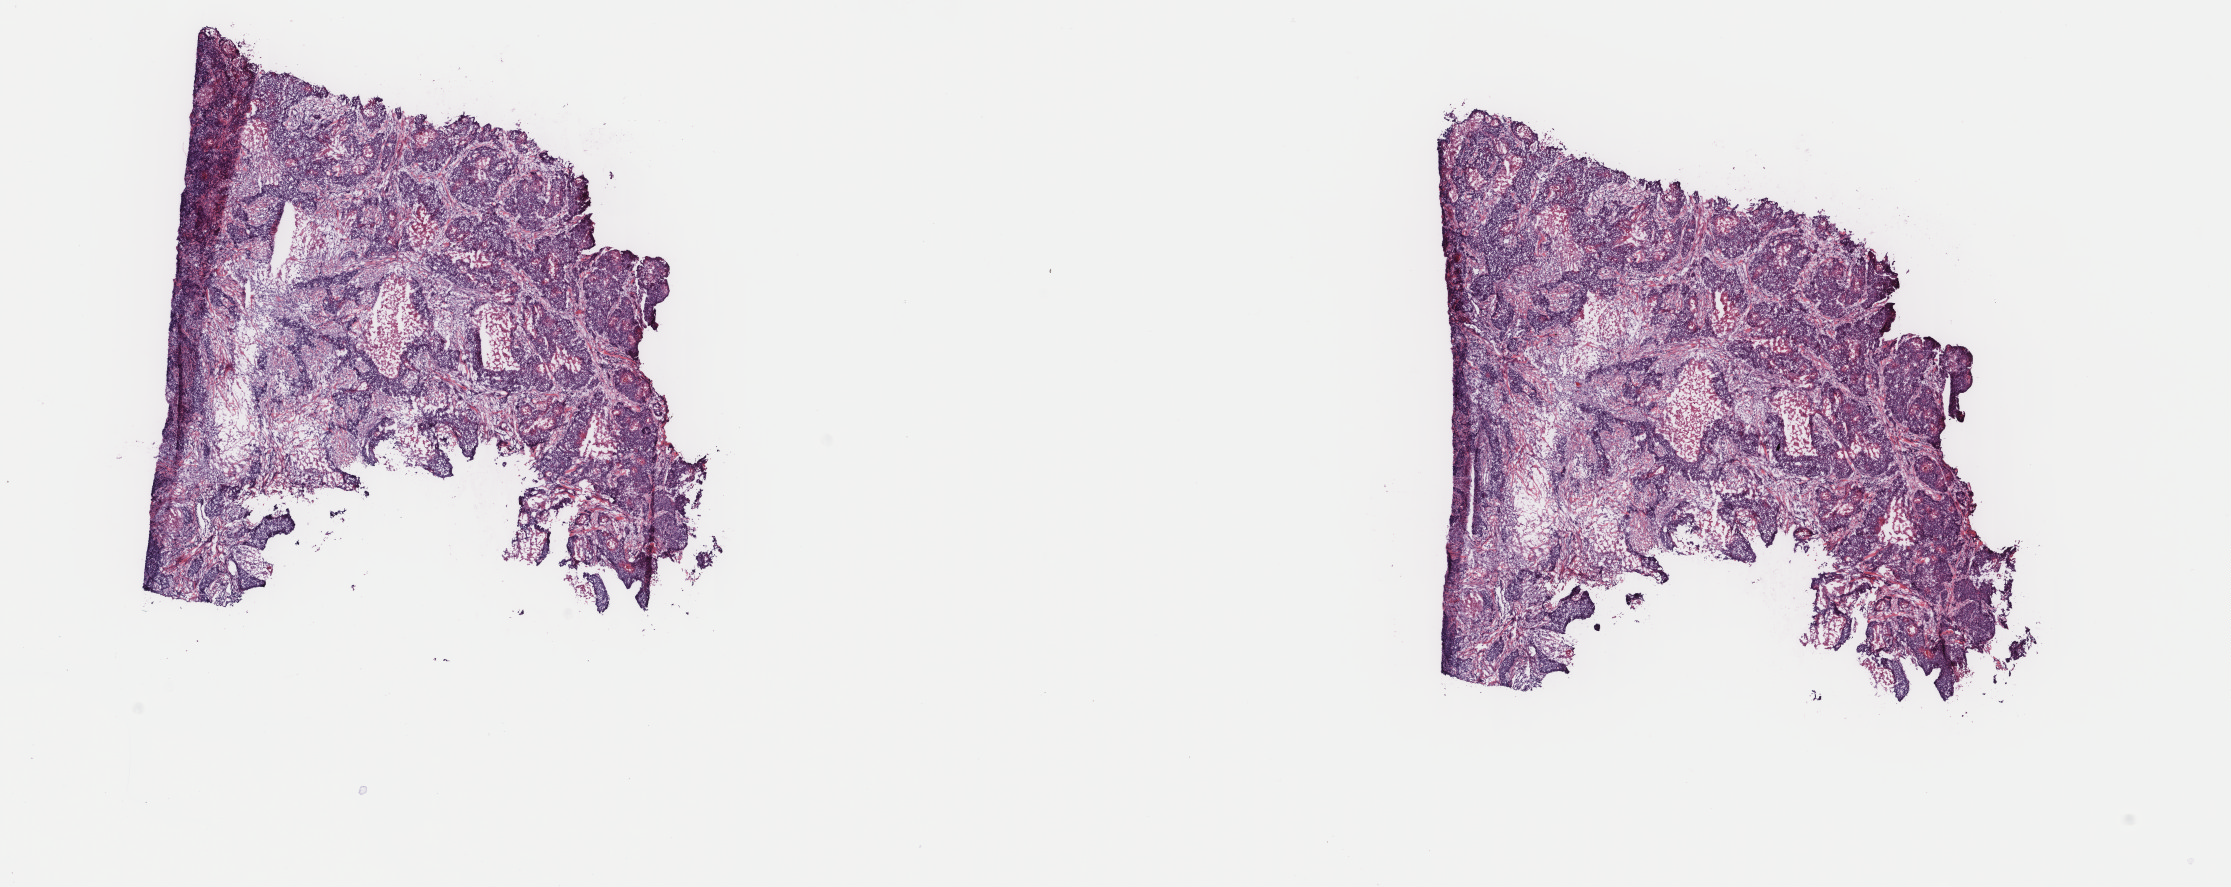
Whole-slide histology image, H&E-stained — whole scanned area (about 17.7 x 7.0 mm, slide scanned at 40x) shown as a low-resolution overview. Frozen section from the top of the tissue portion. Primary tumour sample from the head and neck. Patient: male, age at initial diagnosis 58 years. Pathologist review of this section (percent, as recorded): tumour cells 50%, tumour nuclei 60%.
Diagnosis: Squamous cell carcinoma, NOS.